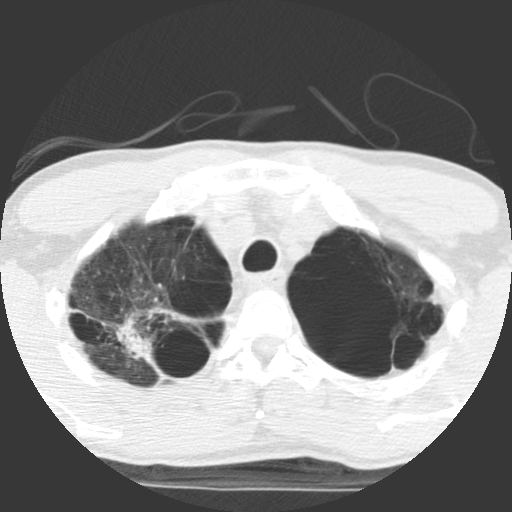
Axial slice from a low-dose chest CT screening exam; baseline screening round; lung window (W 1500 / L -600 HU); 2.5 mm slice thickness; slice 94 of 117 in the series. Male, age 62 years at enrolment. Current smoker at enrolment.
• Expert reader's lesion annotation, box from (x=113, y=308) to (x=214, y=388) px.
• Screening reader's record for this exam: no non-calcified nodule ≥4 mm recorded.
• Official screen result: negative screen, minor abnormalities not suspicious for lung cancer.